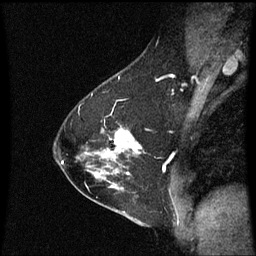
Breast MRI (dynamic contrast-enhanced), one sagittal slice. Slice 40 of 60 in the series (ordered by position). Dynamic contrast-enhanced series, image 2 of 3 at this slice position (ordered by acquisition). 1.5 T. TE 4.2 ms, TR 8.9 ms. 2 mm slice thickness. 256 × 256 image matrix, field of view 200 × 200 mm. Female patient, age 54 years. Case-level facts recorded for this patient, not image findings: setting: breast cancer imaged before/during neoadjuvant chemotherapy; receptor status: HER2-positive.
Structures marked on this image (semi-automatically segmented with operator editing):
- analysis volume of interest (the breast-tissue region the enhancement analysis was run in; not a lesion): bounding box (x1, y1, x2, y2) in pixels: (102, 126, 144, 169)
- tumour enhancement mask (voxels above the 70 % enhancement threshold inside the analysis volume of interest): (114, 130, 142, 153)